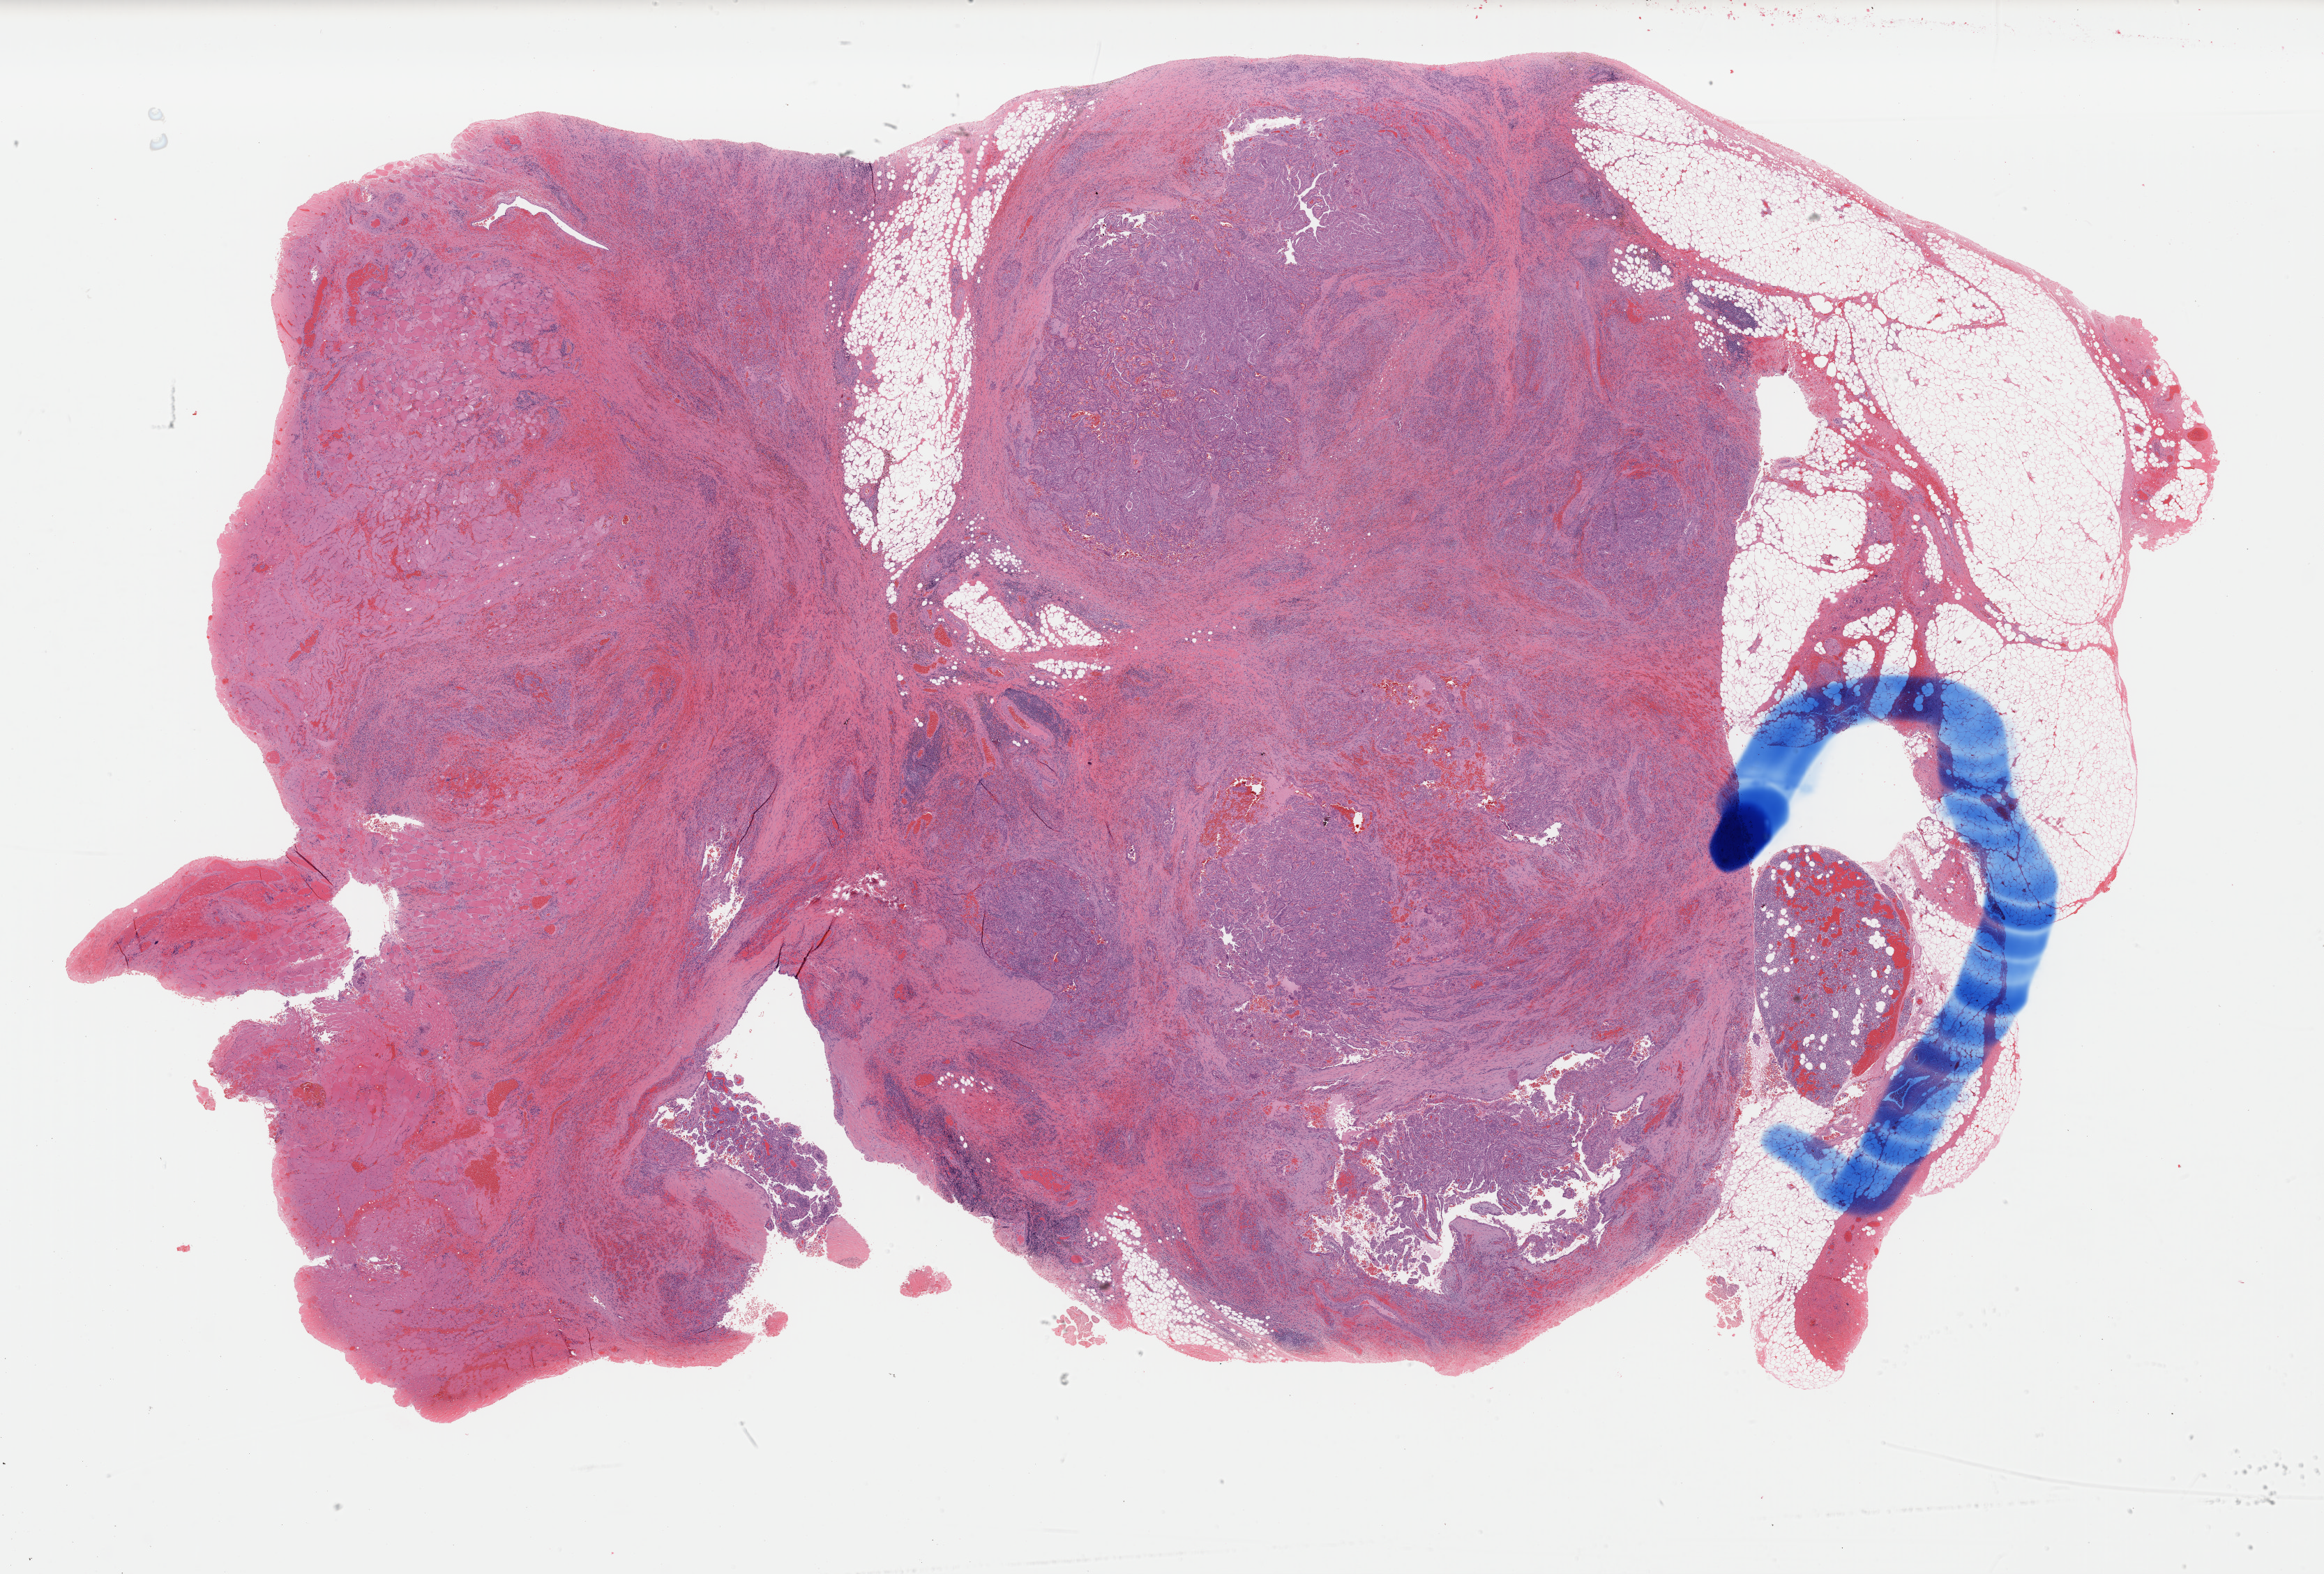
H&E-stained whole-slide image — a low-resolution overview of the entire scanned area, about 26.3 x 17.8 mm (slide scanned at 40x), FFPE section, sample: primary tumour, thyroid. Female, age 34 years at initial diagnosis.
AJCC pathologic stage: I (6th edition). Diagnosis: Papillary adenocarcinoma, NOS.